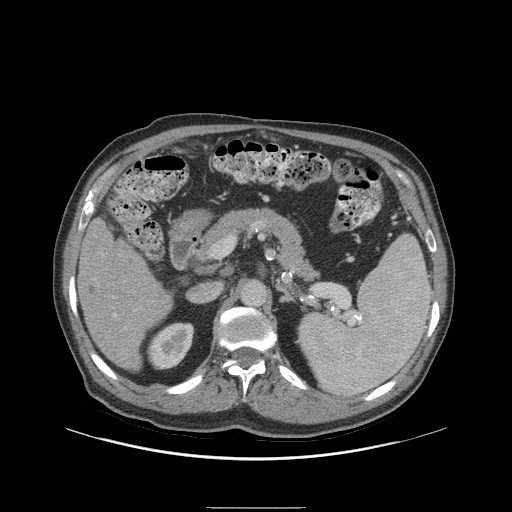
Contrast-enhanced abdominal CT (liver protocol), one axial slice. Position 46 of 105 along the scan axis. Reconstruction kernel STANDARD. 140 kVp. Soft-tissue window (W 400 / L 40 HU). 2.5 mm slice thickness. 512 × 512 image matrix, field of view 440 × 440 mm. Case-level facts recorded for this patient, not image findings: diagnosis: hepatocellular carcinoma (patient treated with transarterial chemoembolisation; whether this scan precedes or follows treatment is not stated here); TNM stage (as recorded): Stage-I; Child-Pugh class: A; tumour nodularity: uninodular; tumour size: 5.1 cm.
Annotated regions visible in this slice (semi-automatic segmentation, software-assisted and operator-edited):
- liver parenchyma outside the tumour (the mass and vessels are separate outlines, so this box may not span the whole liver): bounding box (x1, y1, x2, y2) in pixels: (78, 218, 172, 370)
- liver vessels: (115, 314, 117, 316)